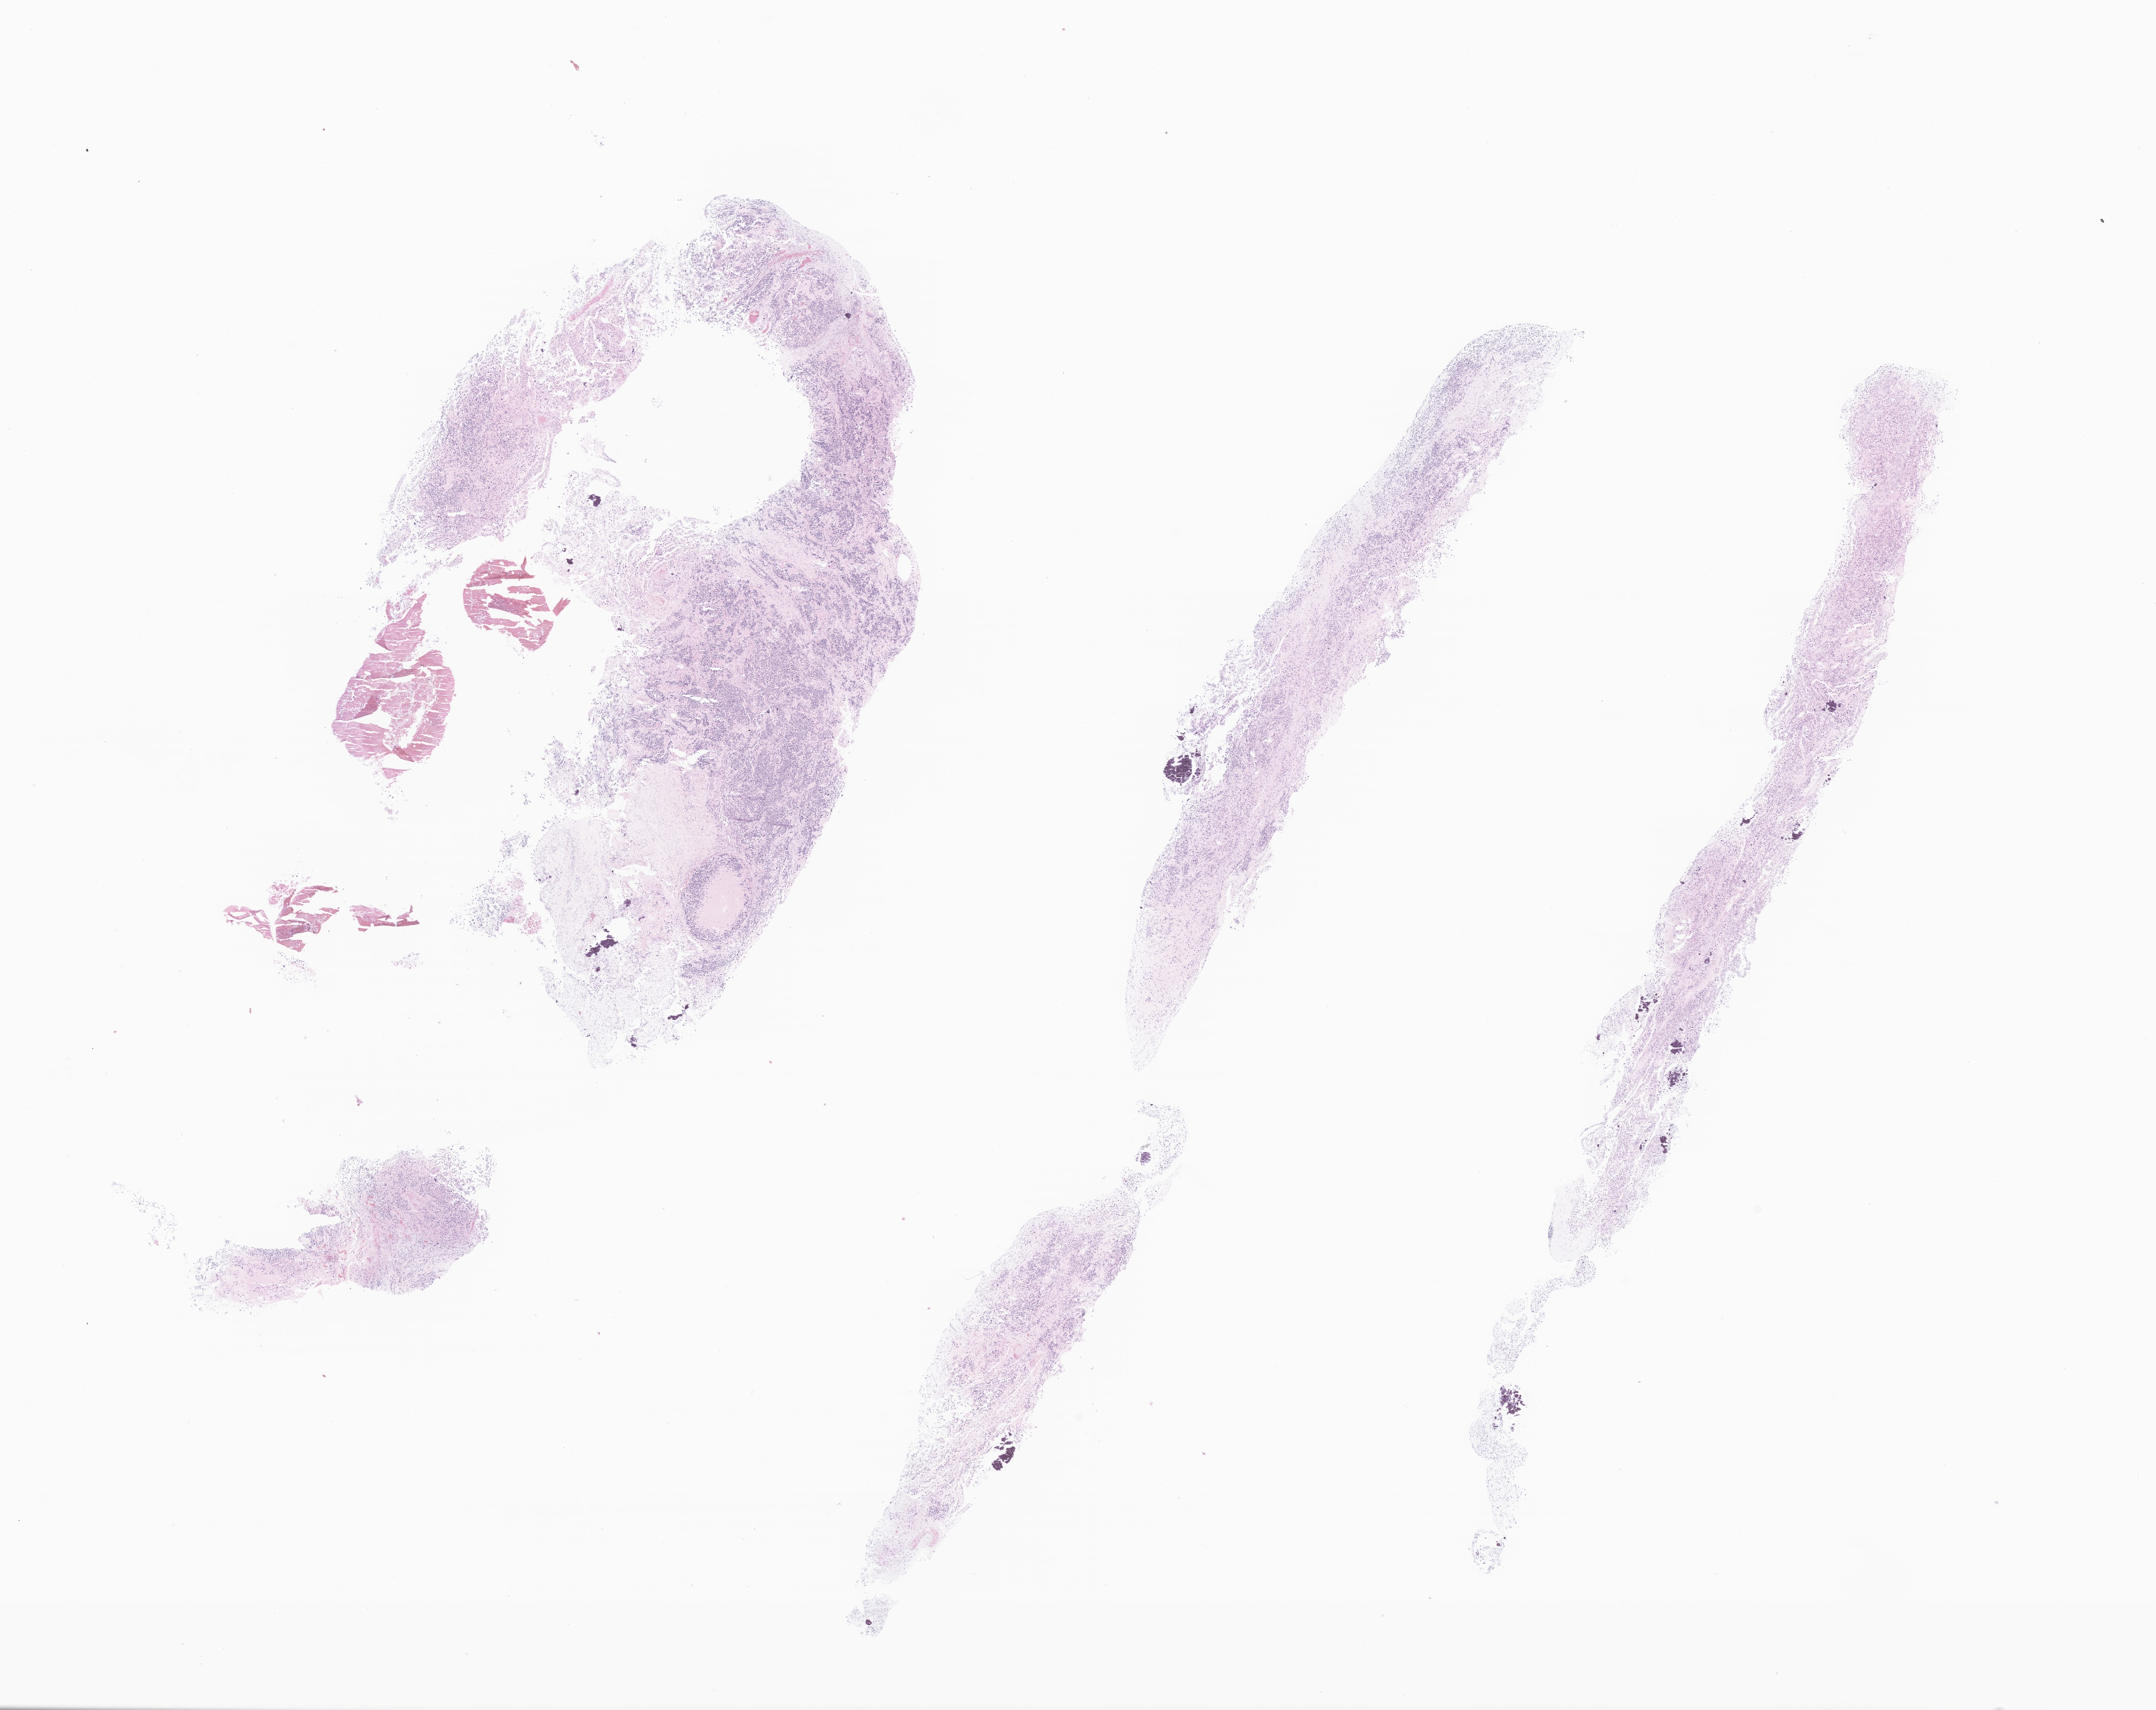
Whole-slide image, haematoxylin and eosin stain of tumor tissue from the retroperitoneum — shown as a low-resolution overview of the whole scanned area (about 20.5 x 16.3 mm); FFPE section. Patient female; age 347 days.
Diagnosis (ICD-O-3 morphology term): Neuroblastoma, NOS.